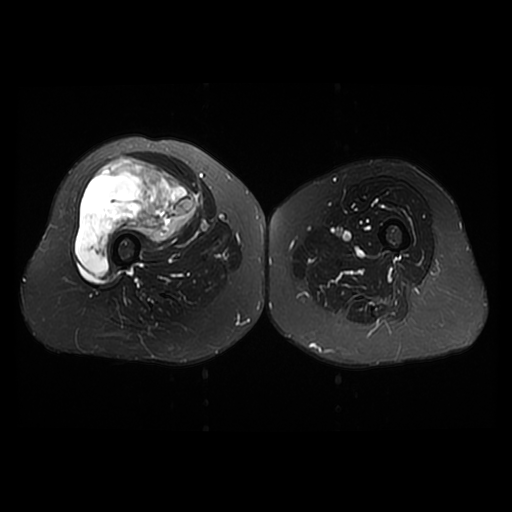
MRI of an extremity soft-tissue mass, one axial slice; position 22 of 42 along the scan axis; T2-weighted fat-saturated; 6 mm slice thickness; 512 × 512 image matrix, field of view 440 × 440 mm. Female patient. Case-level facts recorded for this patient, not image findings: histological type: pleiomorphic undifferentiated sarcoma; grade: high; site of the primary tumour: right quadricep.
Outlined on this slice (expert manual segmentation):
- gross tumour volume including surrounding oedema: box from (x=74, y=156) to (x=197, y=277) px
- gross tumour volume (mass): (x=74, y=156)–(x=197, y=277)